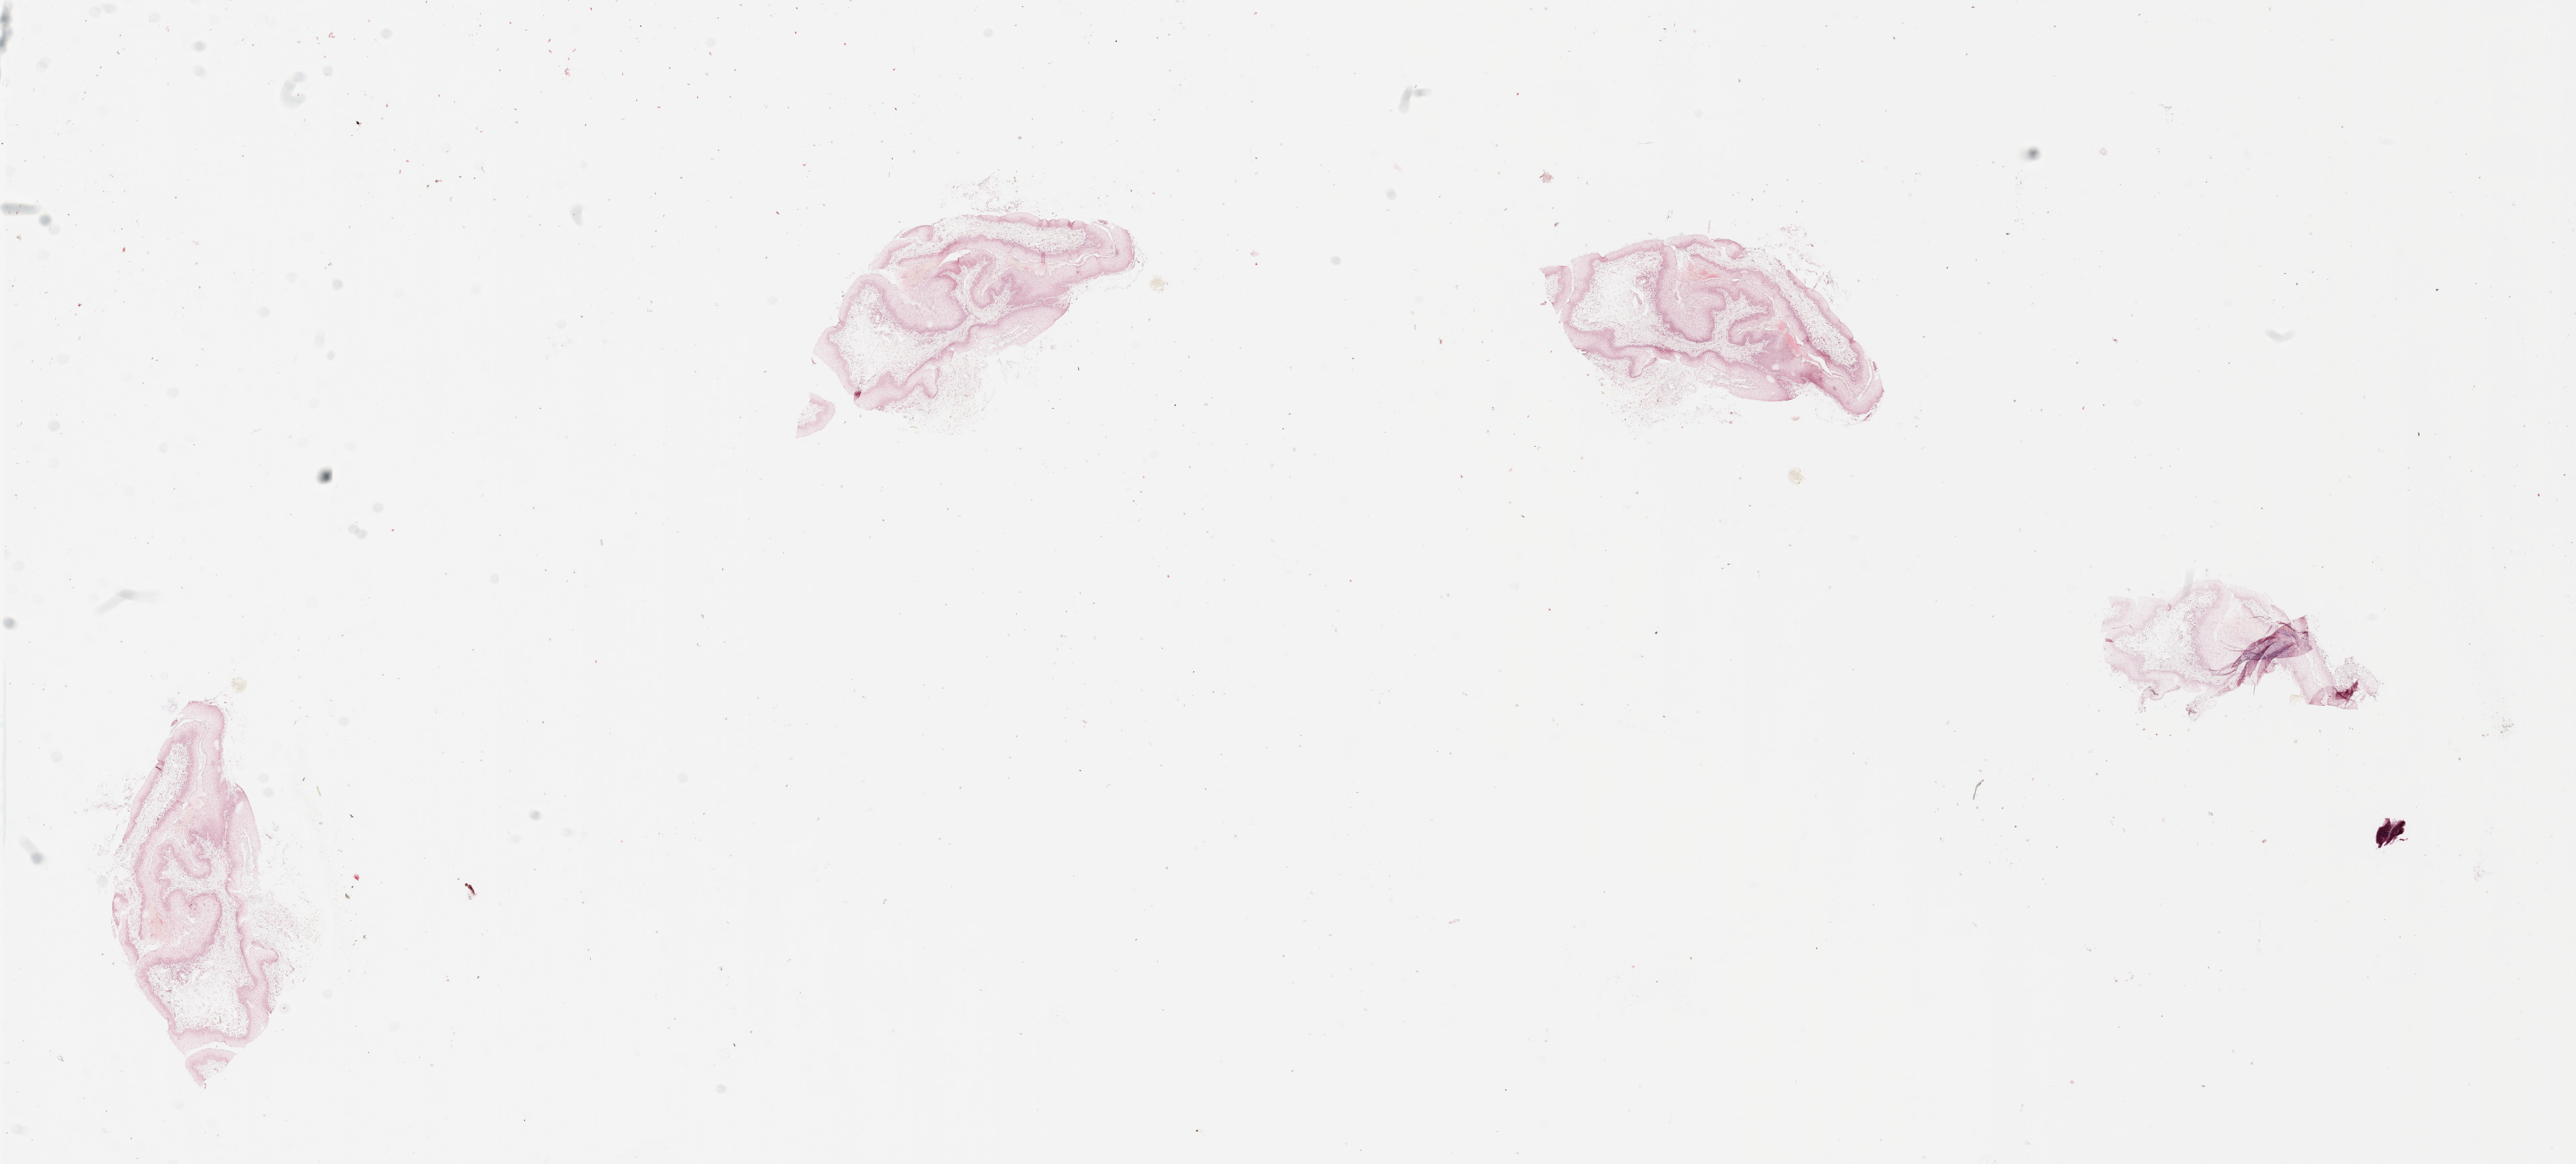
Hematoxylin and eosin (H&E) stained whole-slide image — shown as a low-resolution overview of the whole scanned area (about 30.5 x 13.8 mm, acquisition: 20x scan). Normal (non-tumour) tissue sample, sampled site: larynx. 63-year-old male patient.
- this section: normal (non-tumour) tissue from the same patient
- patient diagnosis: Squamous cell carcinoma, NOS (larynx, NOS)